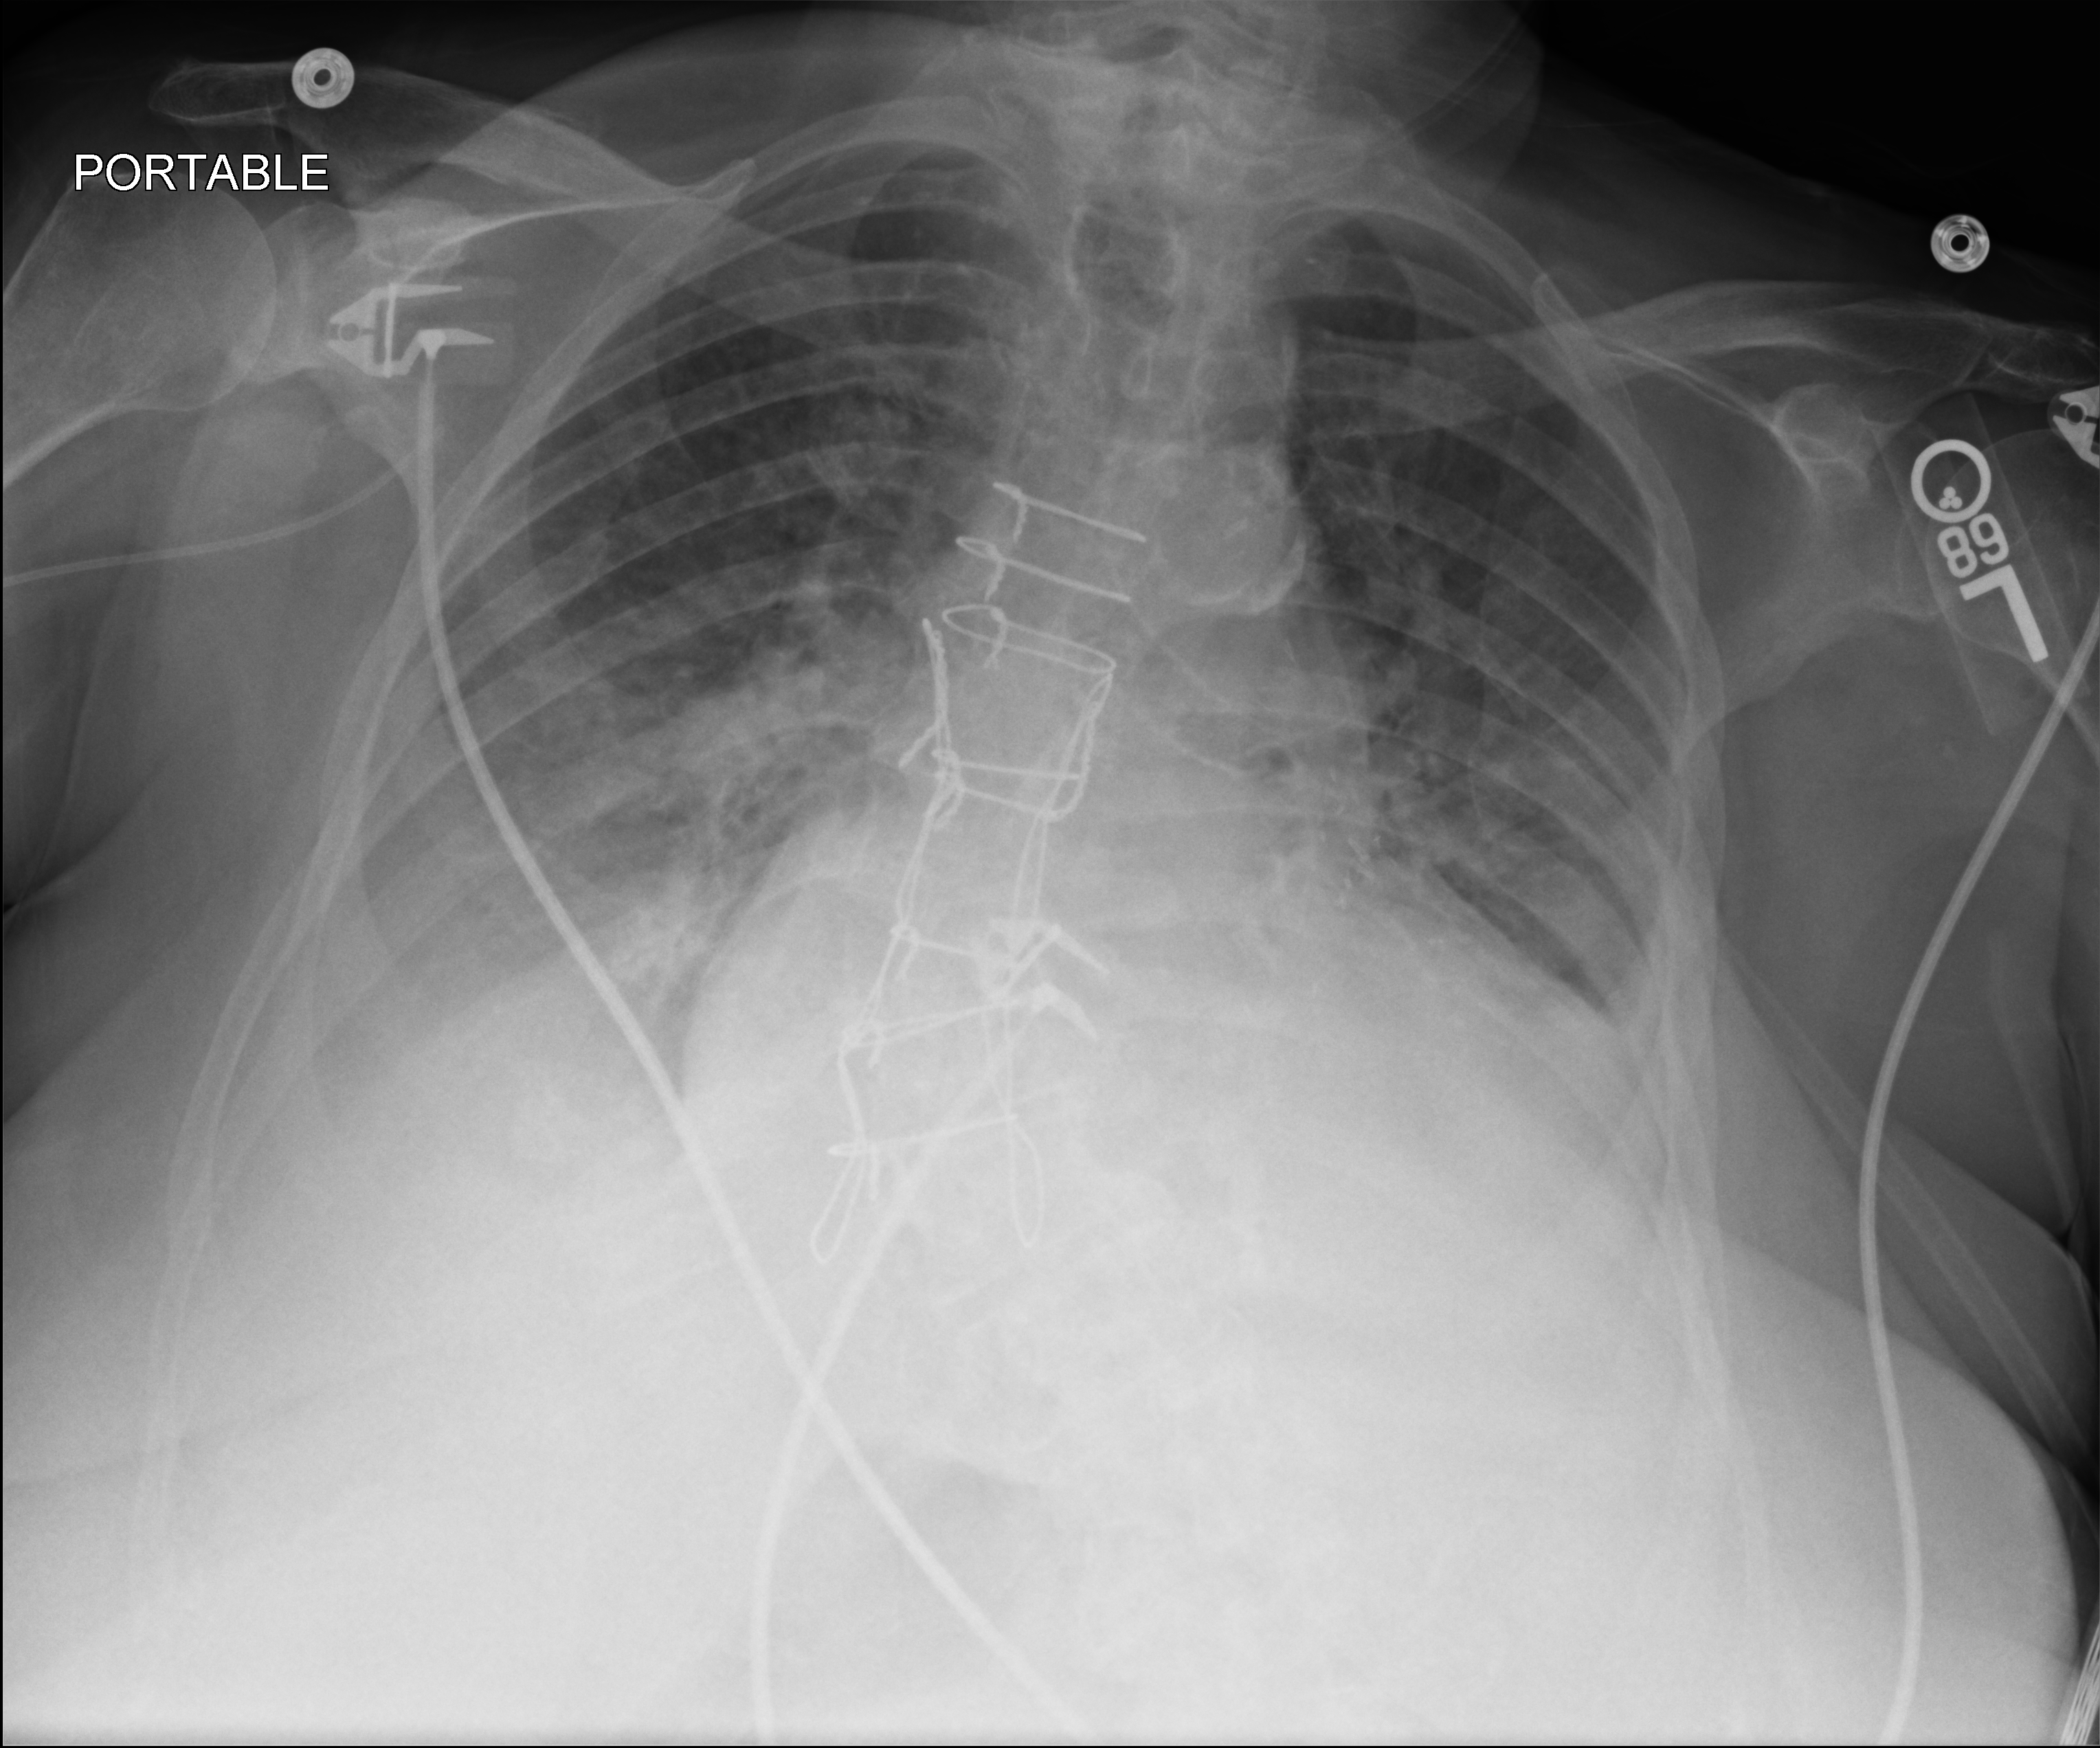
Chest X-ray (portable). Female patient hospitalised with COVID-19, age 75–90 years.
Hospital-stay facts (about this admission, not read from this image; timing relative to this image not recorded):
- length of hospital stay: 10 days
- admitted to intensive care during this hospital stay: no